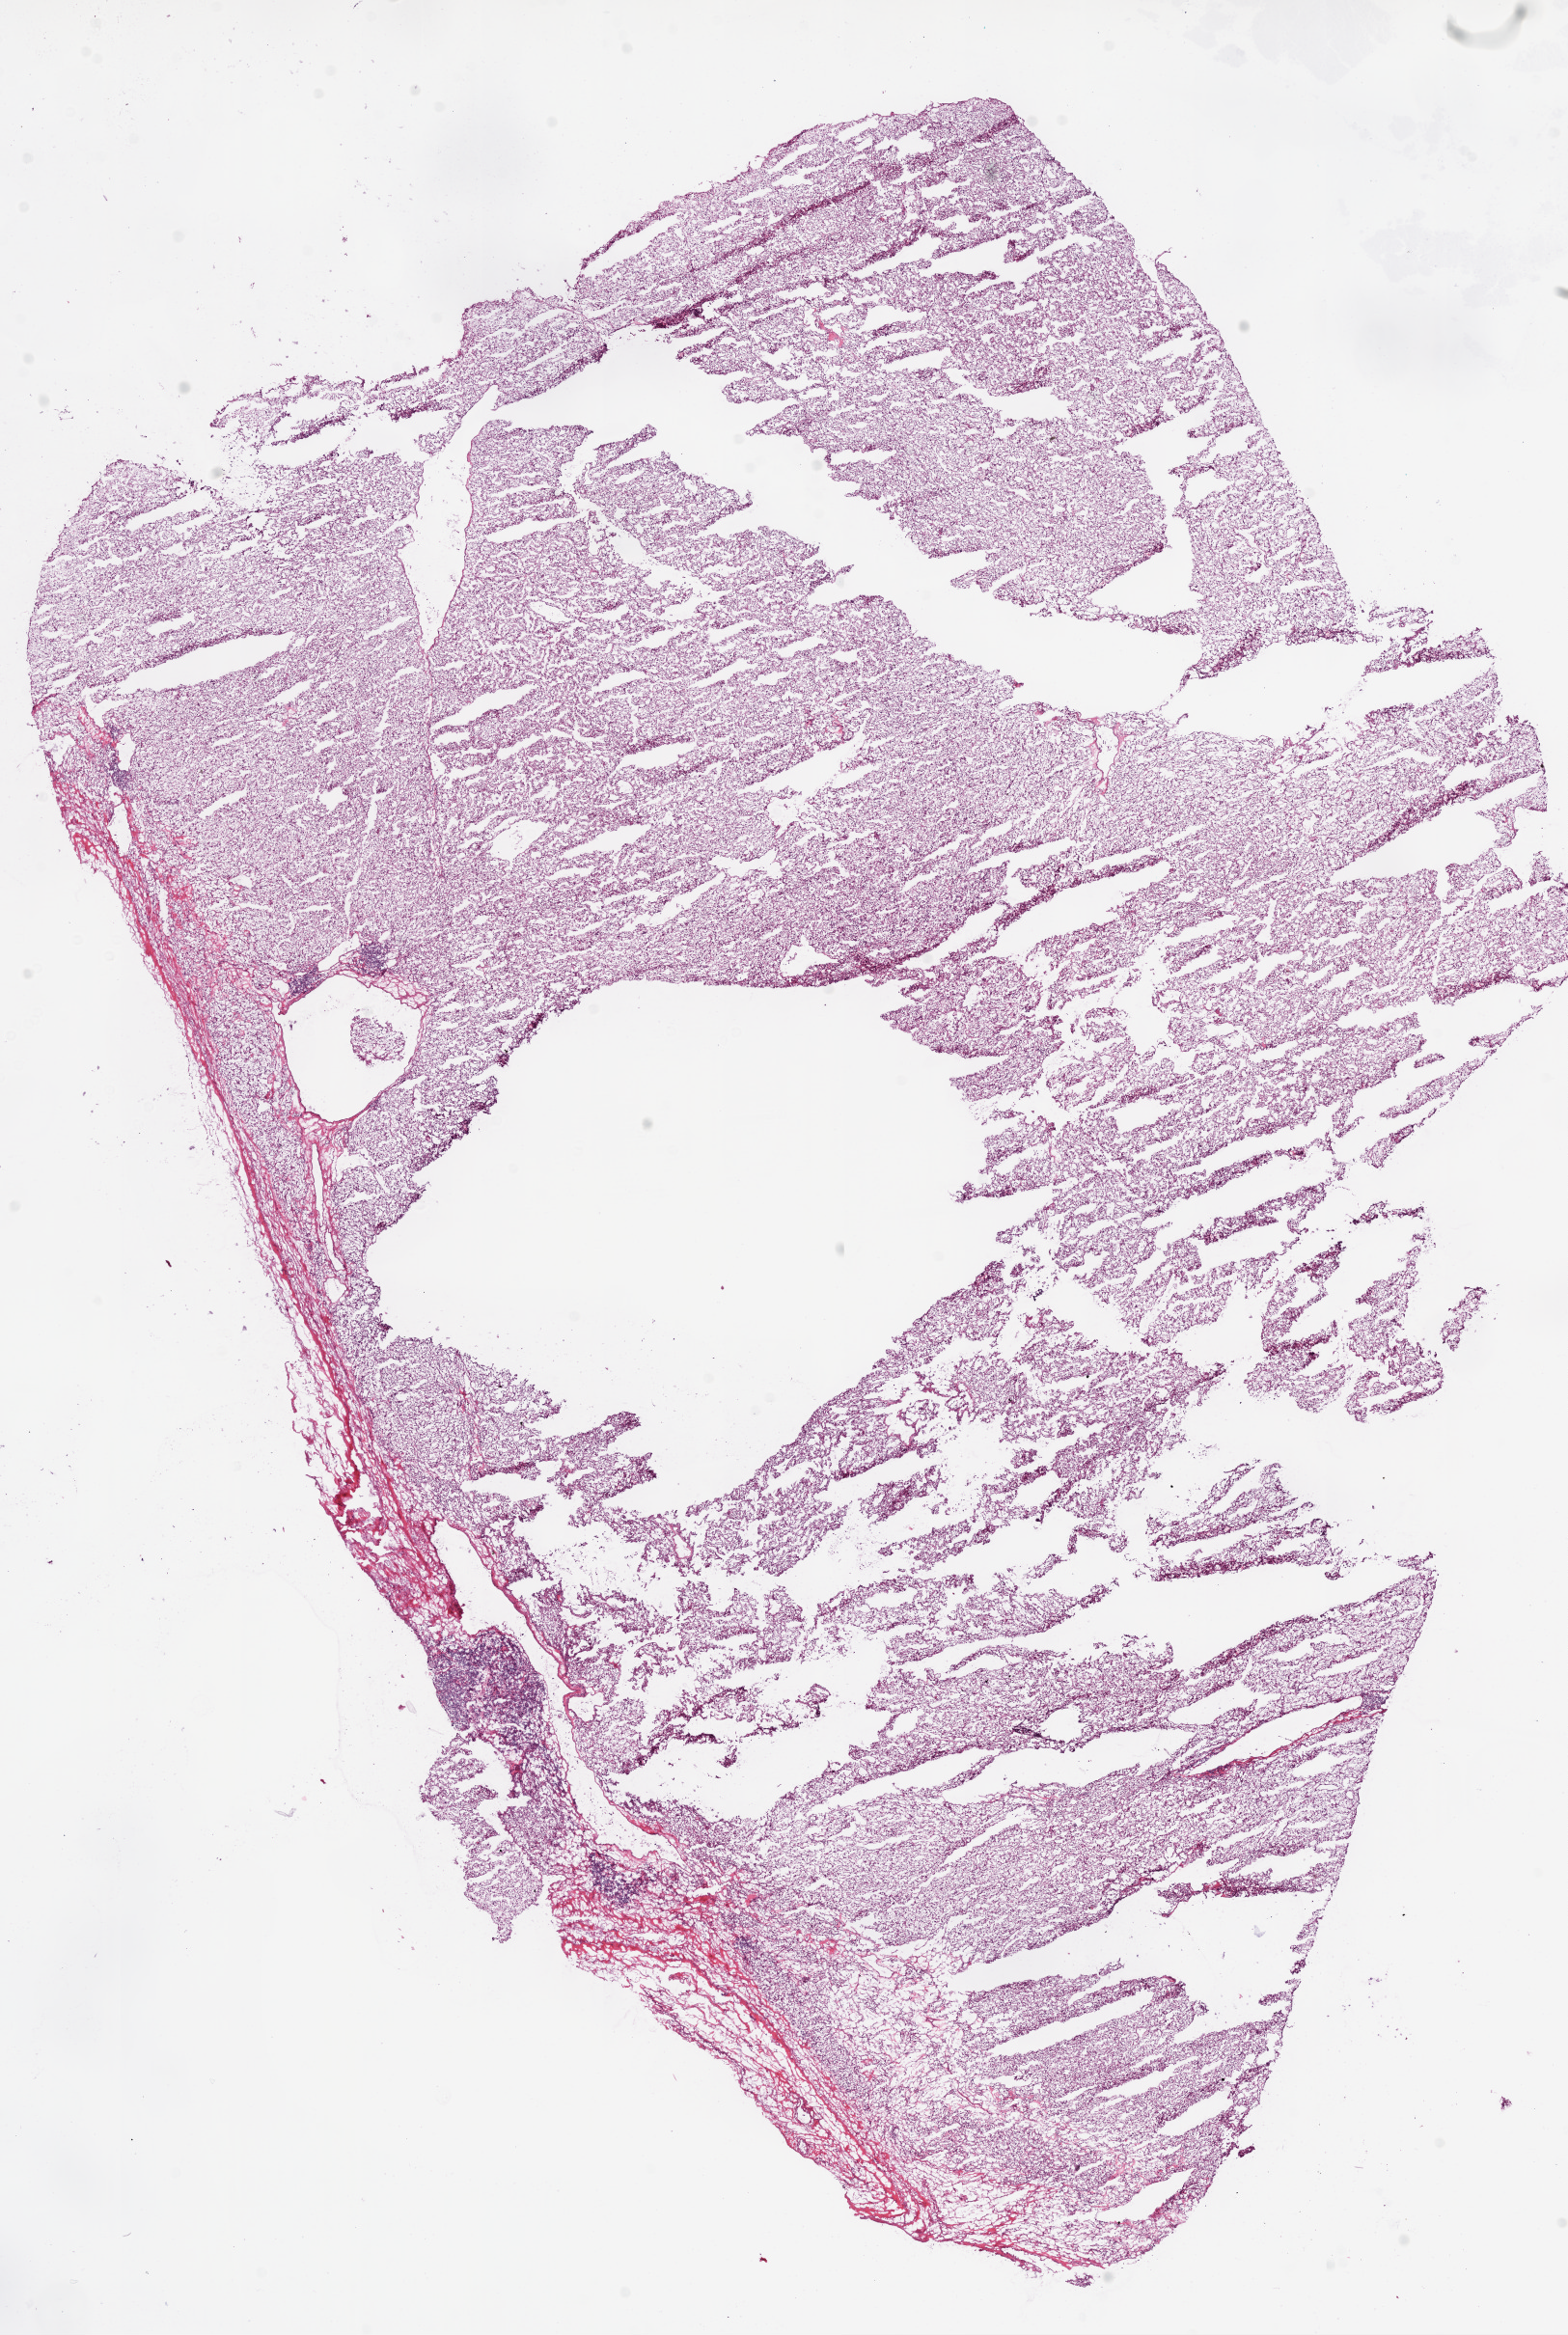
Digitized Hematoxylin and eosin (H&E) stained tissue section (whole slide), low-resolution overview of the scanned area, about 13.0 x 19.4 mm; frozen section; sample: primary tumour, kidney. Patient: female, age at initial diagnosis 65 years. Histologic grade: G2 (moderately differentiated). Composition of this section per pathologist review: tumour cells 95%, tumour nuclei 88%, normal cells 0%, stromal cells 5%, necrosis 0%.
AJCC pathologic stage: I. Lymph nodes positive (case pathology): 0 of 3 examined. Pathologic diagnosis: Clear cell adenocarcinoma, NOS.